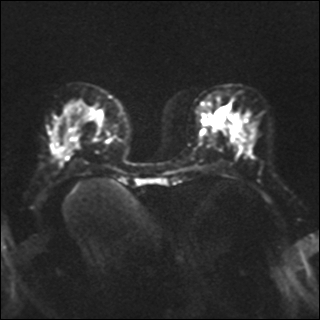
Breast MRI, one axial slice. Slice 12 of 35 in the series (ordered by position). Diffusion-weighted series; image 2 of 4 stored at this slice position (different b-values; order by instance number). 1.5 T. 4 mm slice thickness. 320 × 320 image matrix. Female patient.
Annotated regions visible in this slice (manually delineated by an expert):
- tumour on diffusion-weighted imaging: bounding box [x1, y1, x2, y2] px = [218, 110, 227, 121]